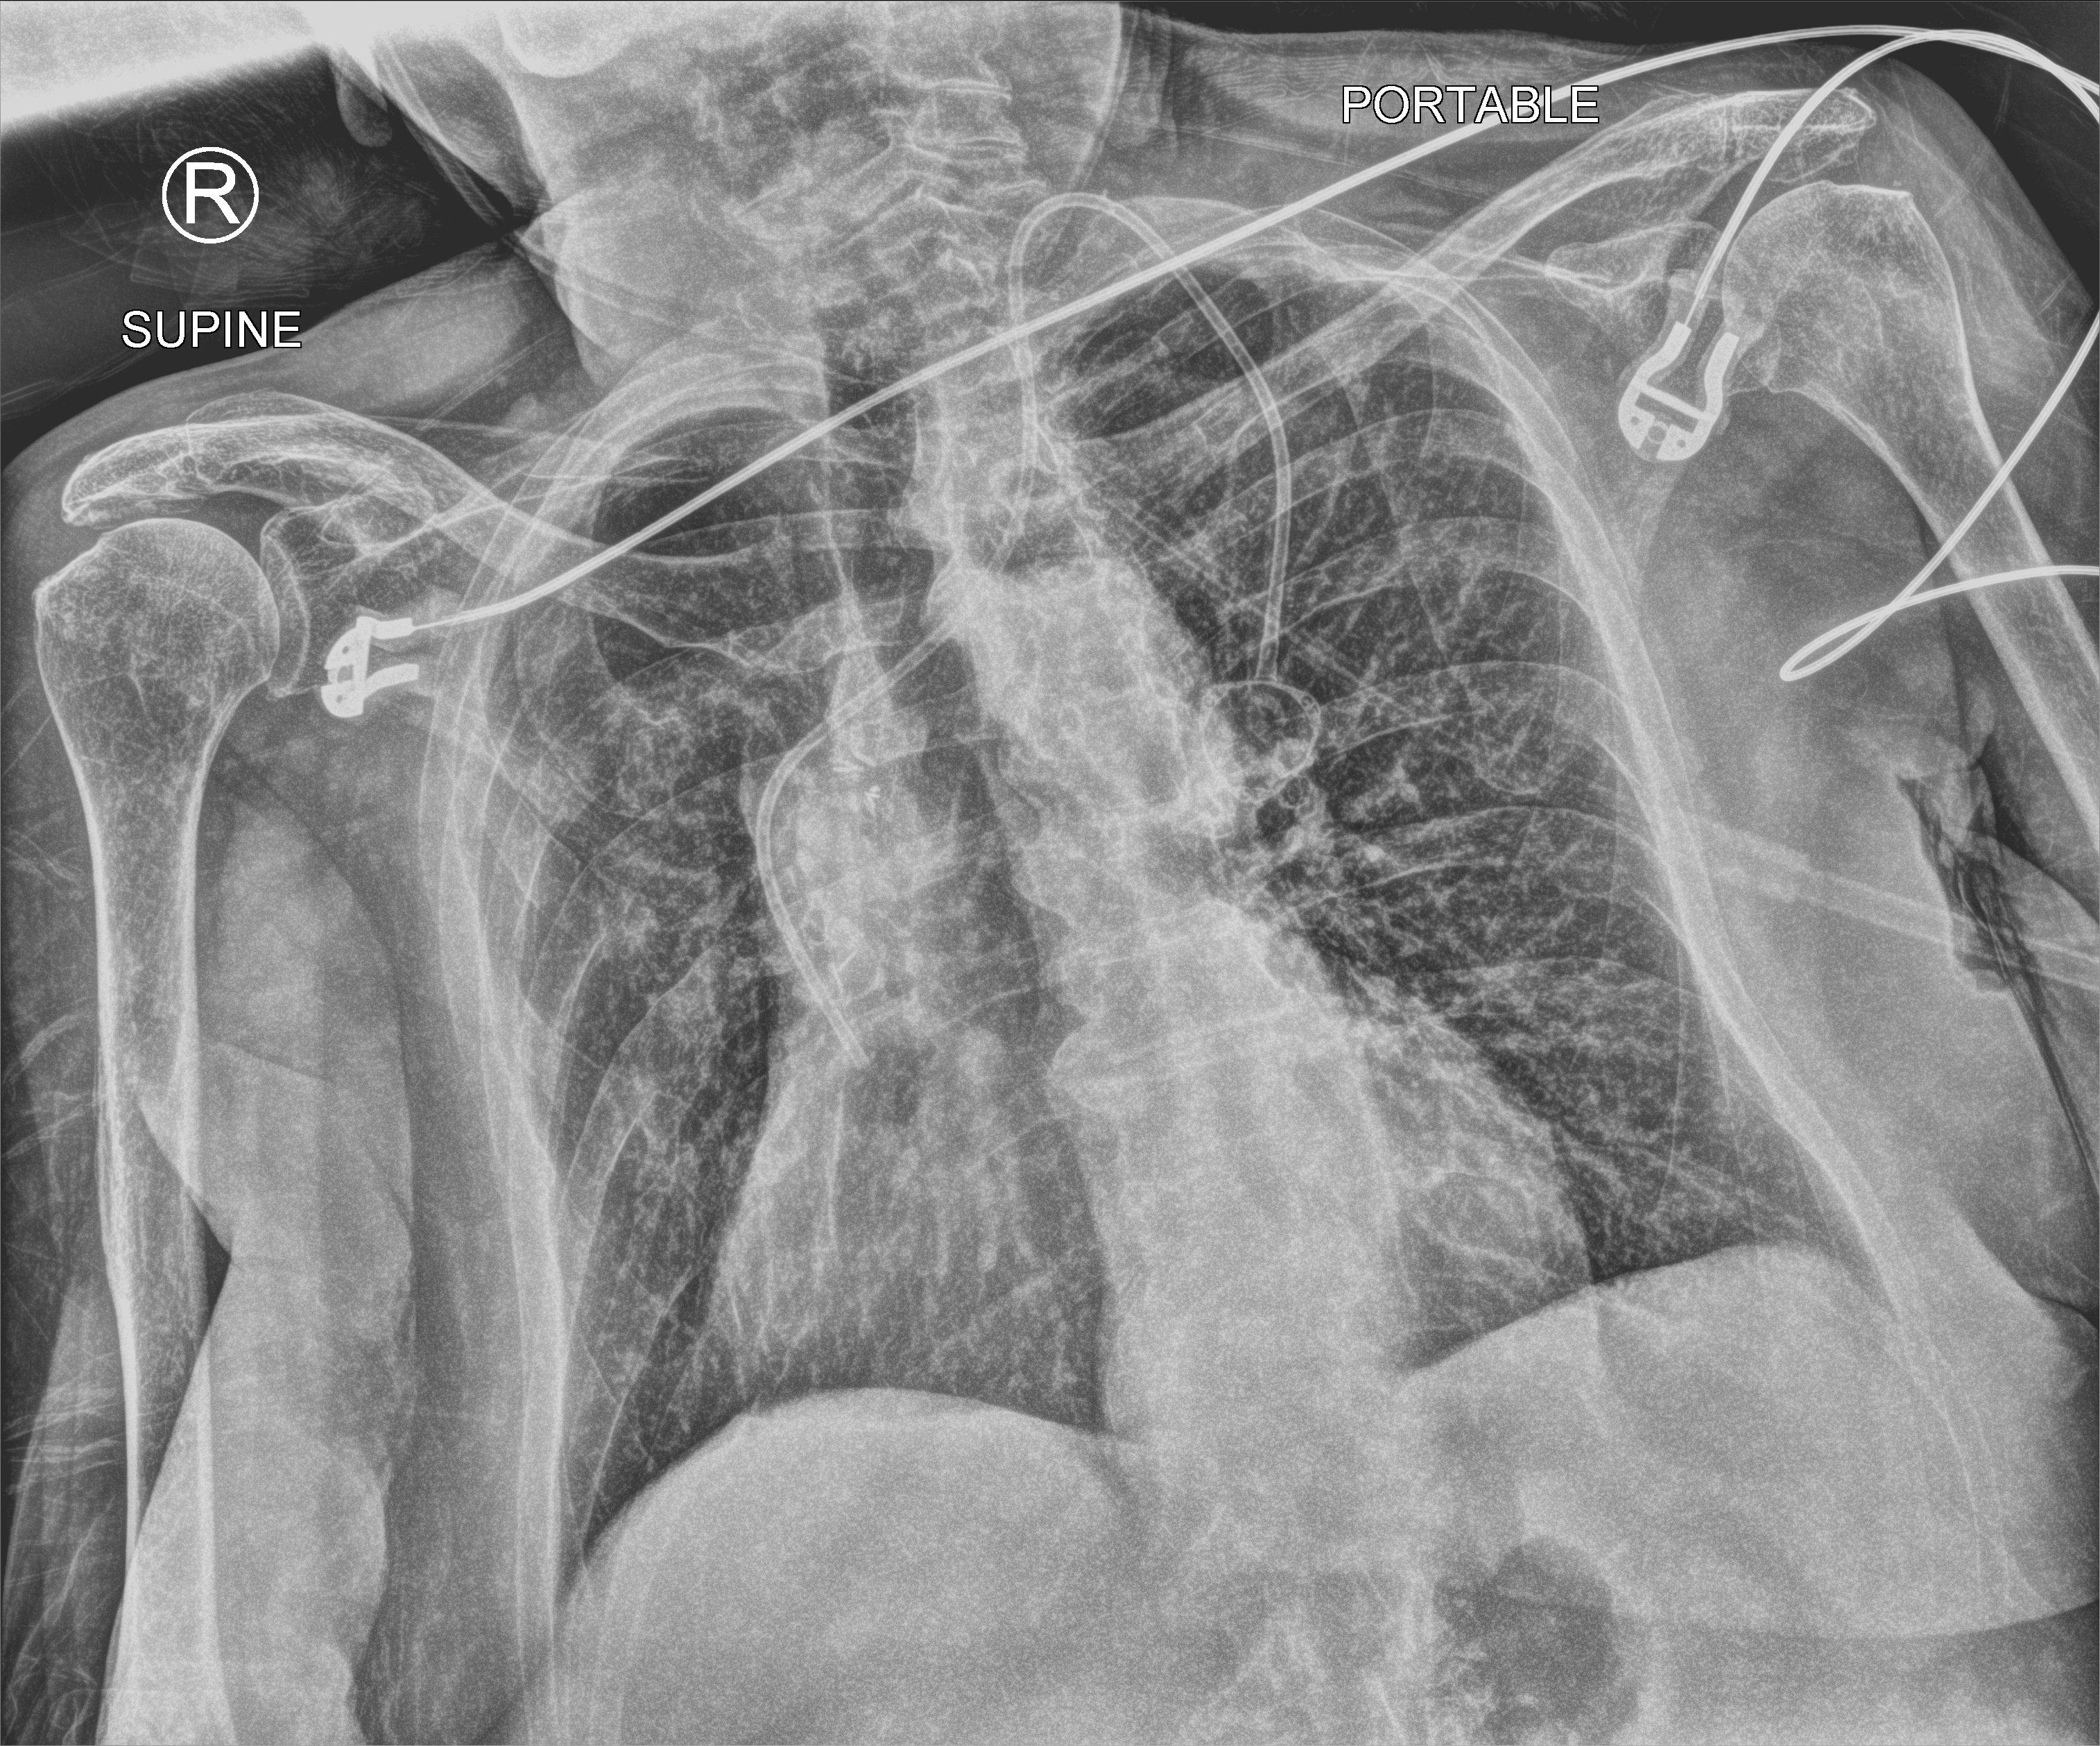
Portable chest radiograph, anteroposterior (AP) projection. Female patient hospitalised with COVID-19, age 75–90 years.
Hospital-stay facts (about this admission, not read from this image; timing relative to this image not recorded):
- admitted to intensive care during this hospital stay: no
- mechanically ventilated during this hospital stay: no